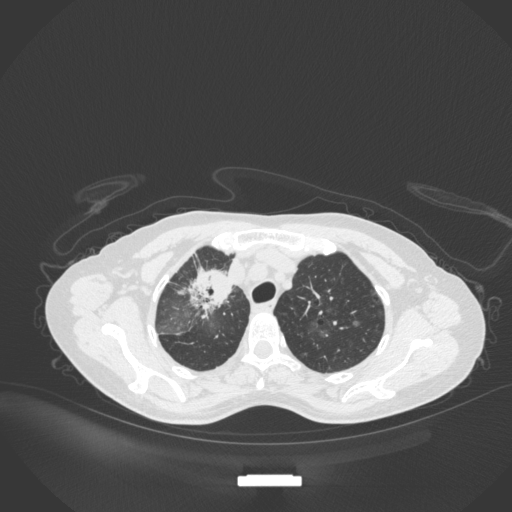
Chest CT, one axial slice; reconstruction kernel B31f; 120 kVp; lung window (W 1500 / L -600 HU); 1 mm slice thickness; 512 × 512 image matrix. Patient: female, 59 years. From the clinical record (not read from this slice): clinical TNM (as recorded): T3 N0 M0; histopathological grade: G1.
Outlined on this slice (bounding box drawn by a radiologist):
- lung tumour (recorded histology: adenocarcinoma): bounding box [x1, y1, x2, y2] px = [181, 259, 231, 319]